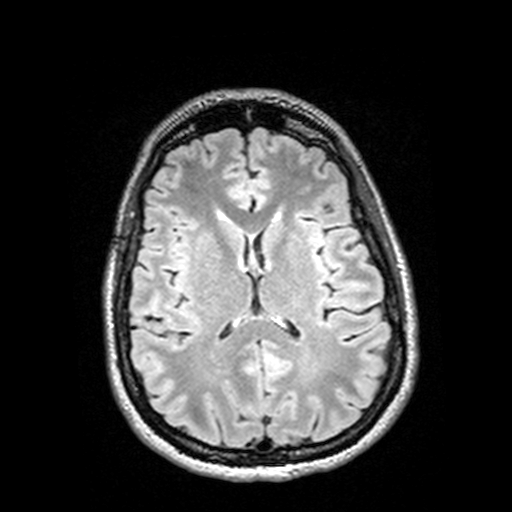
Brain MRI from a brain-tumour surgery series, one axial slice. Position 61 of 144 along the scan axis. T2 FLAIR. 1 mm slice thickness. 512 × 512 image matrix, field of view 250 × 250 mm. From the clinical record (not read from this slice): histopathology: Astrocytoma; WHO grade: 3.
Outlined on this slice (manually delineated by an expert):
- tumour: box from (x=202, y=228) to (x=204, y=230) px